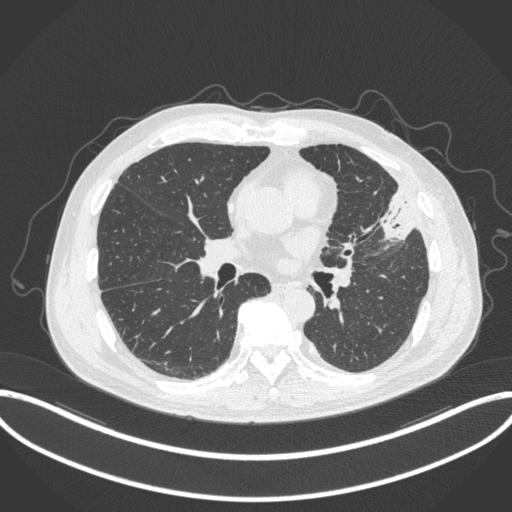
Chest CT, one axial slice. Slice 169 of 382 in the series (ordered by position). Reconstruction kernel B31f. Lung window (W 1500 / L -600 HU). 1 mm slice thickness. 512 × 512 image matrix, field of view 415 × 415 mm. Male patient, age 64 years. From the clinical record (not read from this slice): clinical TNM (as recorded): T4 N1 M0; histopathological grade: G3.
Outlined on this slice (bounding box drawn by a radiologist):
- lung tumour (recorded histology: adenocarcinoma): bounding box (x1, y1, x2, y2) in pixels: (376, 182, 418, 246)